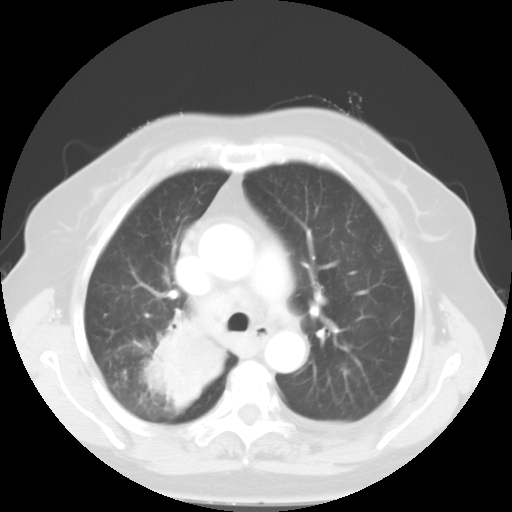
Chest CT, one axial slice; slice 36 of 52 in the series (ordered by position); 120 kVp; lung window (W 1500 / L -600 HU); 512 × 512 image matrix. Patient: female, 81 years. From the clinical record (not read from this slice): clinical TNM (as recorded): T4 N3 M1b.
Structures marked on this image (bounding box drawn by a radiologist):
- lung tumour (recorded histology: adenocarcinoma): bounding box (x1, y1, x2, y2) in pixels: (142, 309, 226, 409)